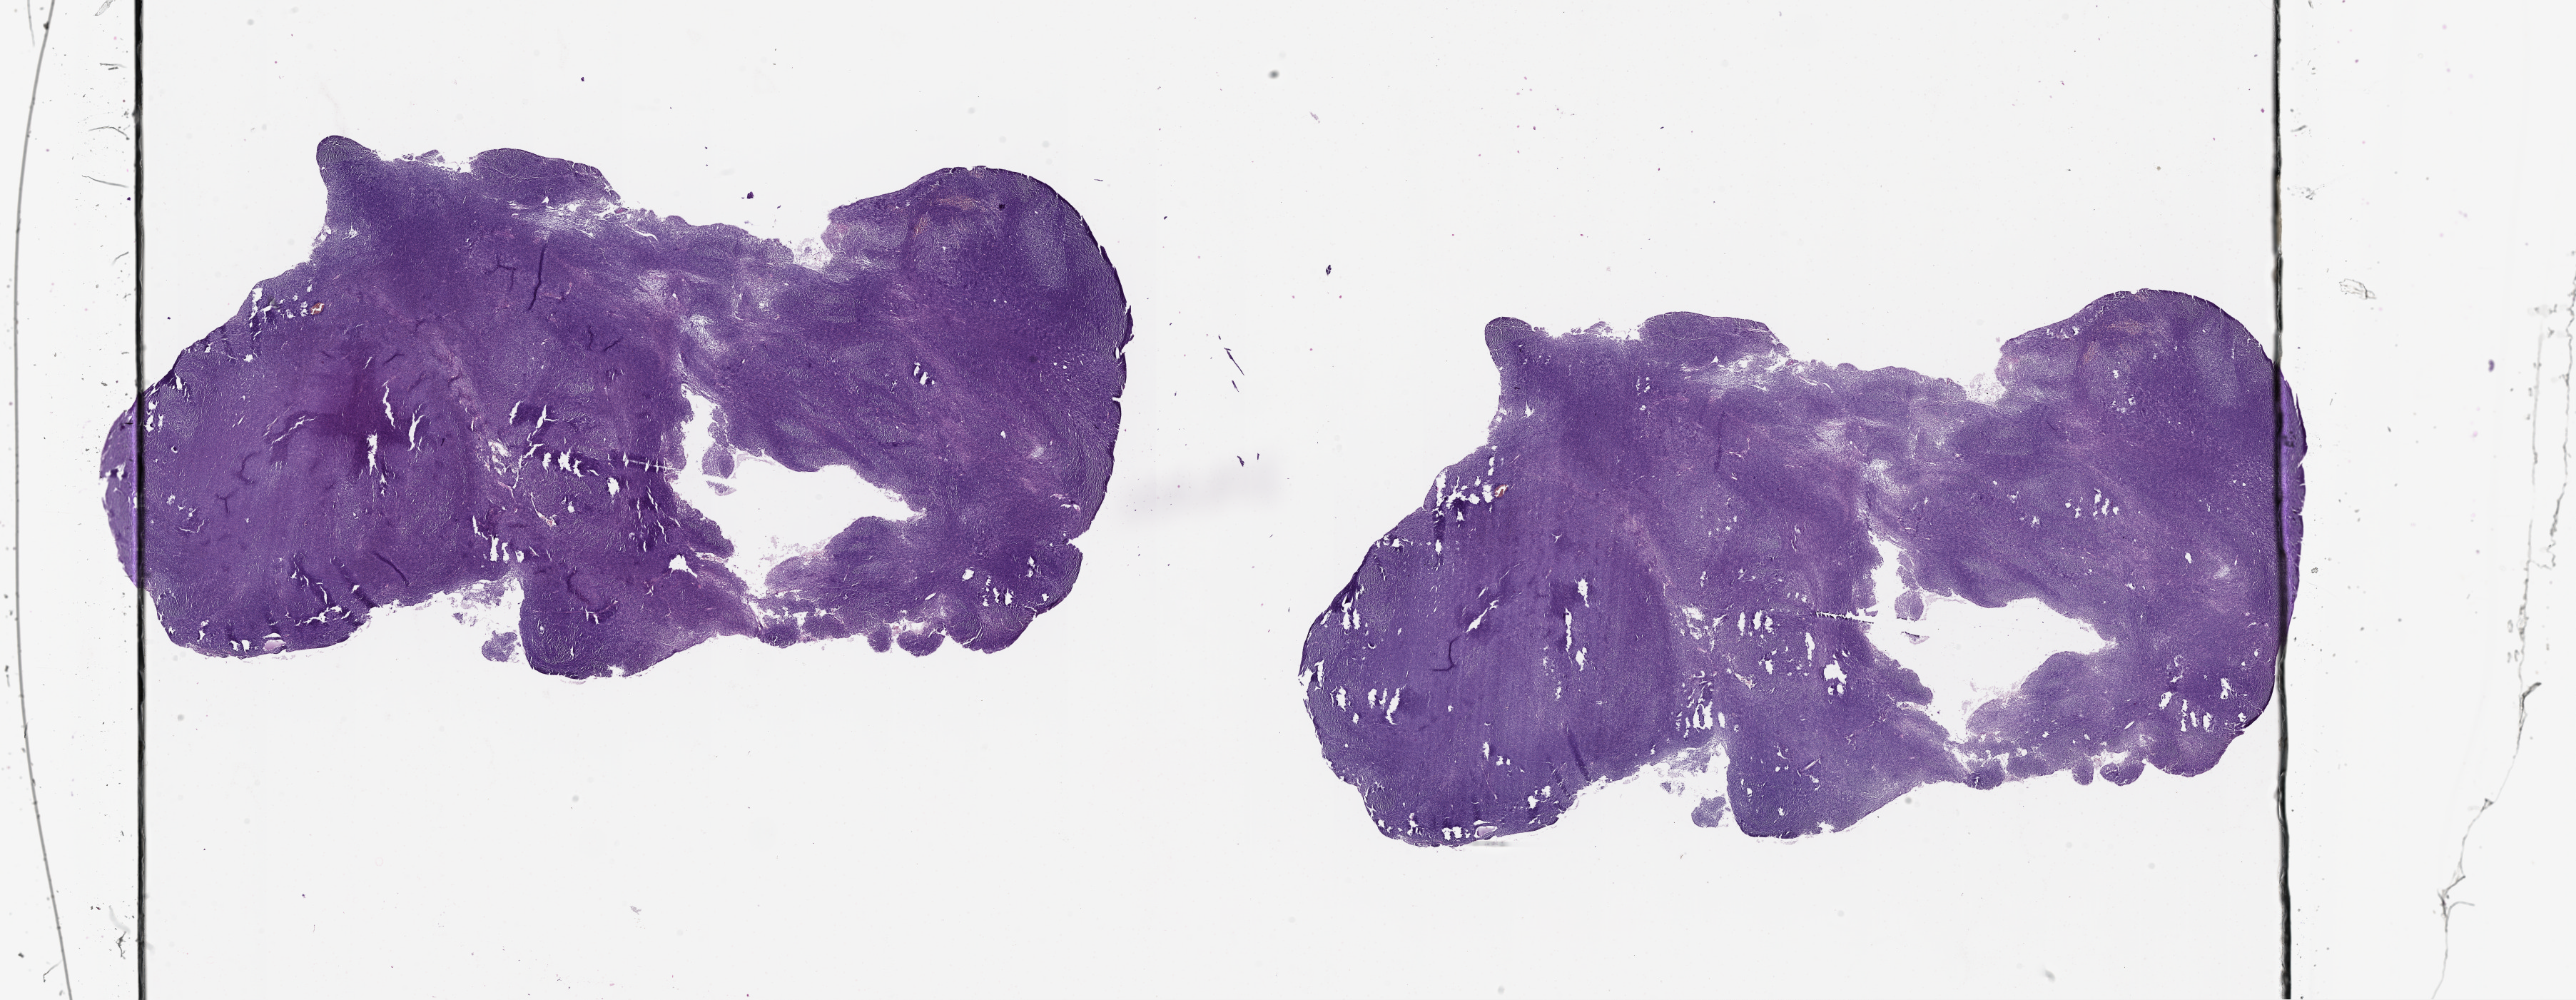
Digitized H&E-stained tissue section (whole slide) — shown as a low-resolution overview of the whole scanned area (about 29.1 x 11.3 mm).
Patient diagnosis (cohort enrolment): sarcoma (site not recorded at cohort level).